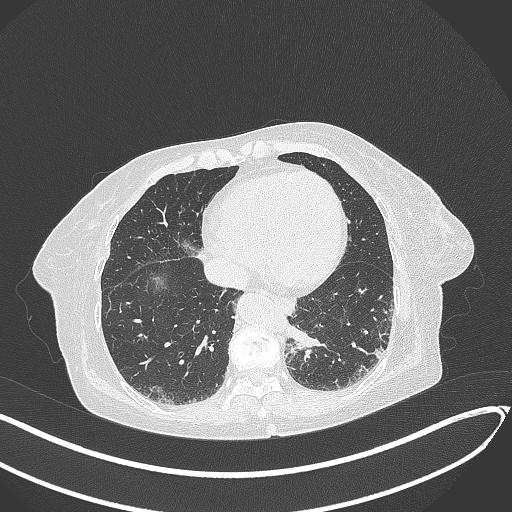
Chest CT, one axial slice; position 61 of 324 along the scan axis; reconstruction kernel B70f; 120 kVp; lung window (W 1500 / L -600 HU); 1 mm slice thickness; 512 × 512 image matrix, field of view 400 × 400 mm. Female patient, age 82 years. Case-level facts recorded for this patient, not image findings: clinical TNM (as recorded): T1b N0 M1.
Annotated regions visible in this slice (bounding box drawn by a radiologist):
- lung tumour (recorded histology: adenocarcinoma): bounding box <288,325,330,350> (left, top, right, bottom; pixels)